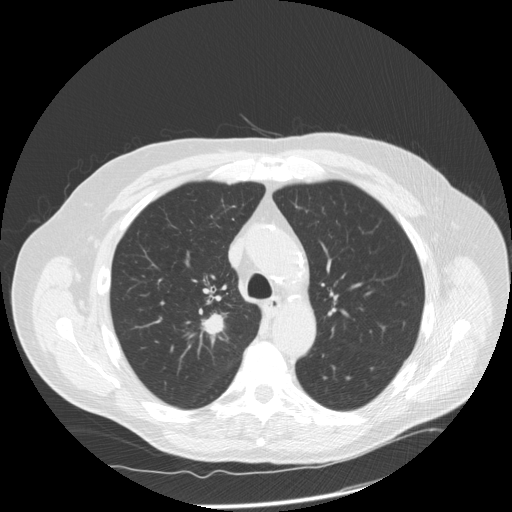
Low-dose screening chest CT, one axial slice; slice 117 of 166 in the series (ordered by position); reconstruction kernel STANDARD; 120 kVp; lung window (W 1500 / L -600 HU); 512 × 512 image matrix, field of view 390 × 390 mm.
Annotated regions visible in this slice (outlined manually by an expert reader):
- lesion 1 (tumor, upper lobe of right lung): box from (x=203, y=314) to (x=223, y=335) px